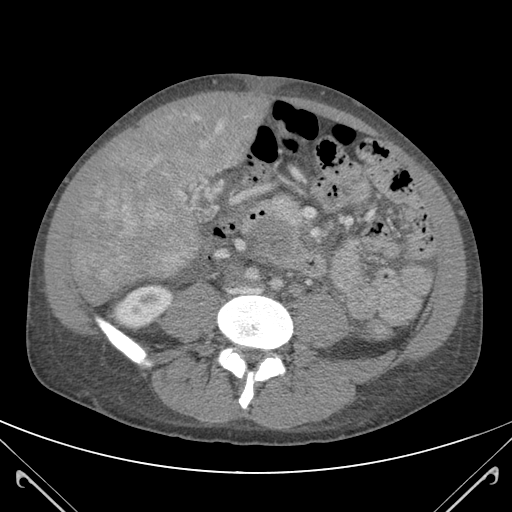
Contrast-enhanced abdominal CT (liver protocol), one axial slice; soft-tissue window (W 400 / L 40 HU); 512 × 512 image matrix, field of view 380 × 380 mm. From the clinical record (not read from this slice): diagnosis: hepatocellular carcinoma (patient treated with transarterial chemoembolisation; whether this scan precedes or follows treatment is not stated here); TNM stage (as recorded): Stage-IIIB.
Annotated regions visible in this slice (semi-automatic segmentation, software-assisted and operator-edited):
- mass: bounding box <85,94,252,271> (left, top, right, bottom; pixels)